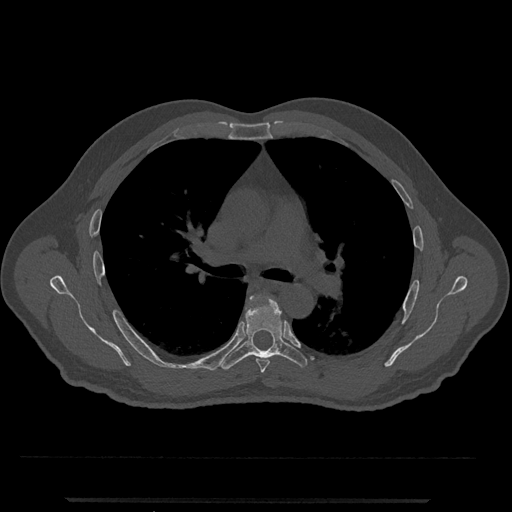
CT including the spine, one axial slice; slice 757 of 797 in the series (ordered by position); reconstruction kernel Br40s/3; 120 kVp; bone window (W 1800 / L 400 HU); 0.5 mm slice thickness; 512 × 512 image matrix, field of view 419 × 419 mm. Patient: male, 63 years. Case-level facts recorded for this patient, not image findings: primary cancer: prostate.
Outlined on this slice (semi-automatic segmentation, software-assisted and operator-edited):
- T5 vertebra: bounding box <246,302,270,373> (left, top, right, bottom; pixels)
- T6 vertebra: <220,295,307,370>